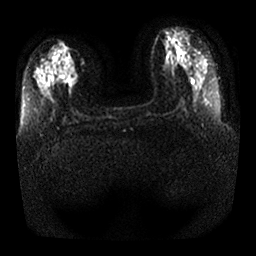
Breast MRI, one axial slice; slice 11 of 25 in the series (ordered by position); diffusion-weighted series; image 2 of 4 stored at this slice position (different b-values; order by instance number); 1.5 T; 256 × 256 image matrix, field of view 350 × 350 mm. Female patient.
Structures marked on this image (manually delineated by an expert):
- tumour on diffusion-weighted imaging: bounding box (x1, y1, x2, y2) in pixels: (64, 62, 78, 83)